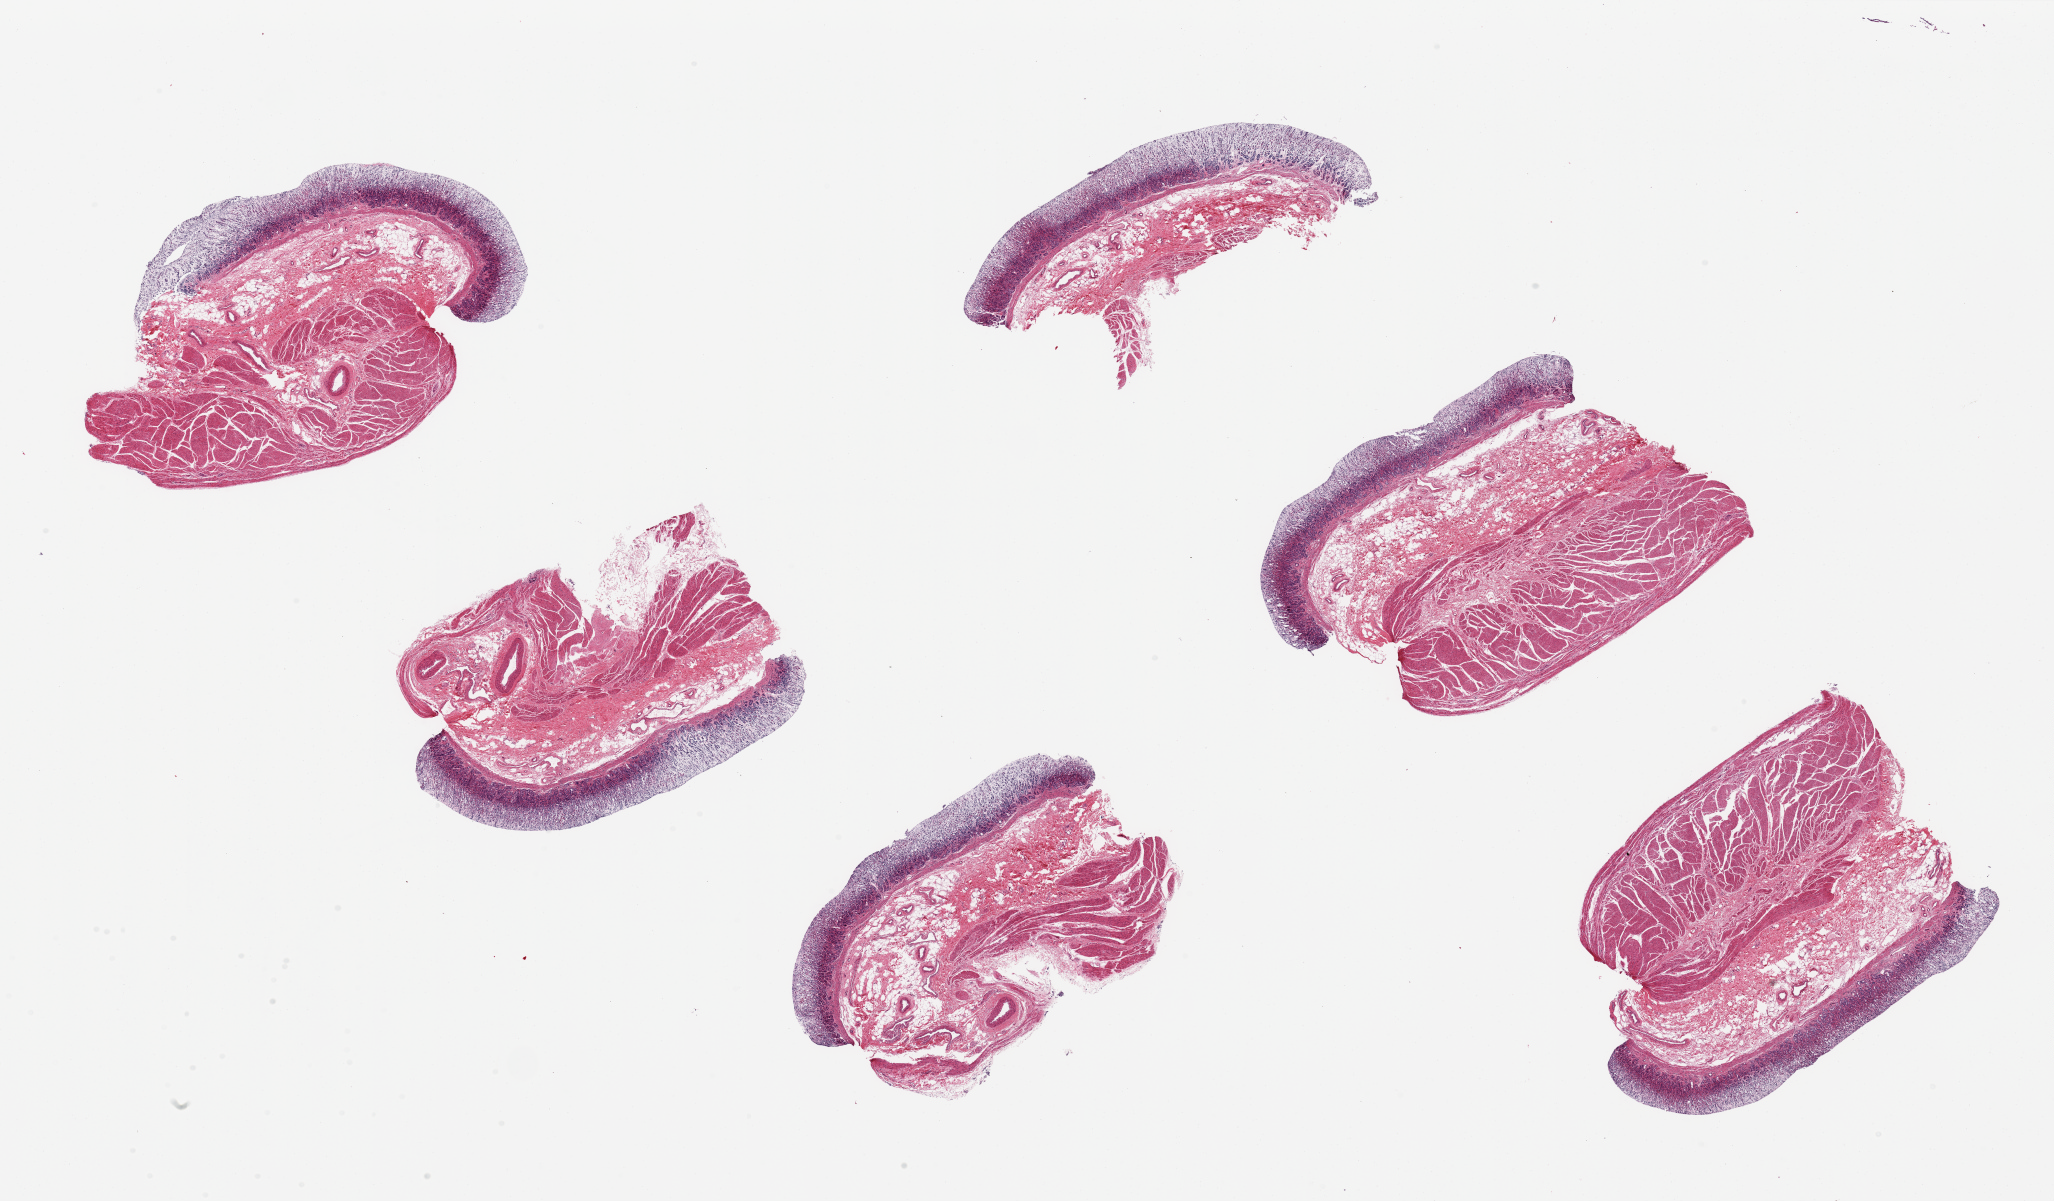
Digitized haematoxylin and eosin-stained section, brightfield — shown as a low-resolution overview of the whole scanned area (about 32.5 x 19.0 mm). PAXgene-fixed, paraffin-embedded tissue. Sampled site (target tissue): stomach. Tissue donor sample. Donor: male.
- review note (as recorded): 6 ~6X3.5mm pieces. Epithelium/mucosa poorly preserved , ~10-20% specimen thickness